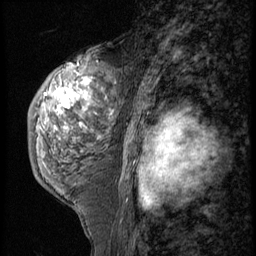
Breast MRI (dynamic contrast-enhanced), one sagittal slice. 3 images stored at this slice position (order not interpretable as contrast timing). 1.5 T. TE 4.2 ms, TR 9 ms. 2.5 mm slice thickness. 256 × 256 image matrix. Patient: female, 50 years. From the clinical record (not read from this slice): setting: breast cancer imaged before/during neoadjuvant chemotherapy; receptor status: triple-negative.
Structures marked on this image (semi-automatically segmented with operator editing):
- analysis volume of interest (the breast-tissue region the enhancement analysis was run in; not a lesion): bounding box (x1, y1, x2, y2) in pixels: (27, 50, 121, 191)
- tumour enhancement mask (voxels above the 140 % enhancement threshold inside the analysis volume of interest): (58, 79, 89, 109)